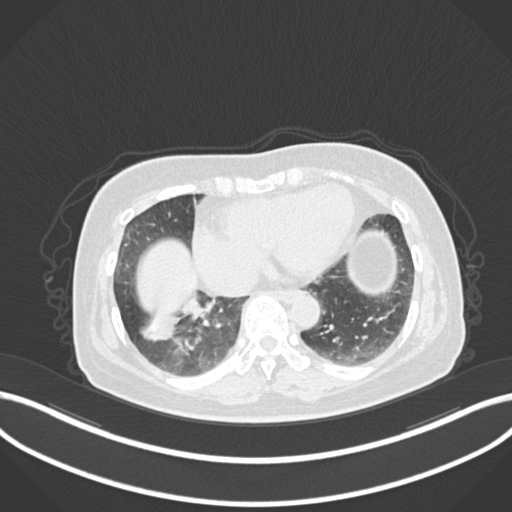
Chest CT, one axial slice. Position 35 of 222 along the scan axis. Lung window (W 1500 / L -600 HU). 1 mm slice thickness. 512 × 512 image matrix, field of view 400 × 400 mm. Female patient, age 67 years. Case-level facts recorded for this patient, not image findings: clinical TNM (as recorded): T1c N1 M0; histopathological grade: G2-3.
Outlined on this slice (bounding box drawn by a radiologist):
- lung tumour (recorded histology: adenocarcinoma): bounding box <136,298,210,344> (left, top, right, bottom; pixels)